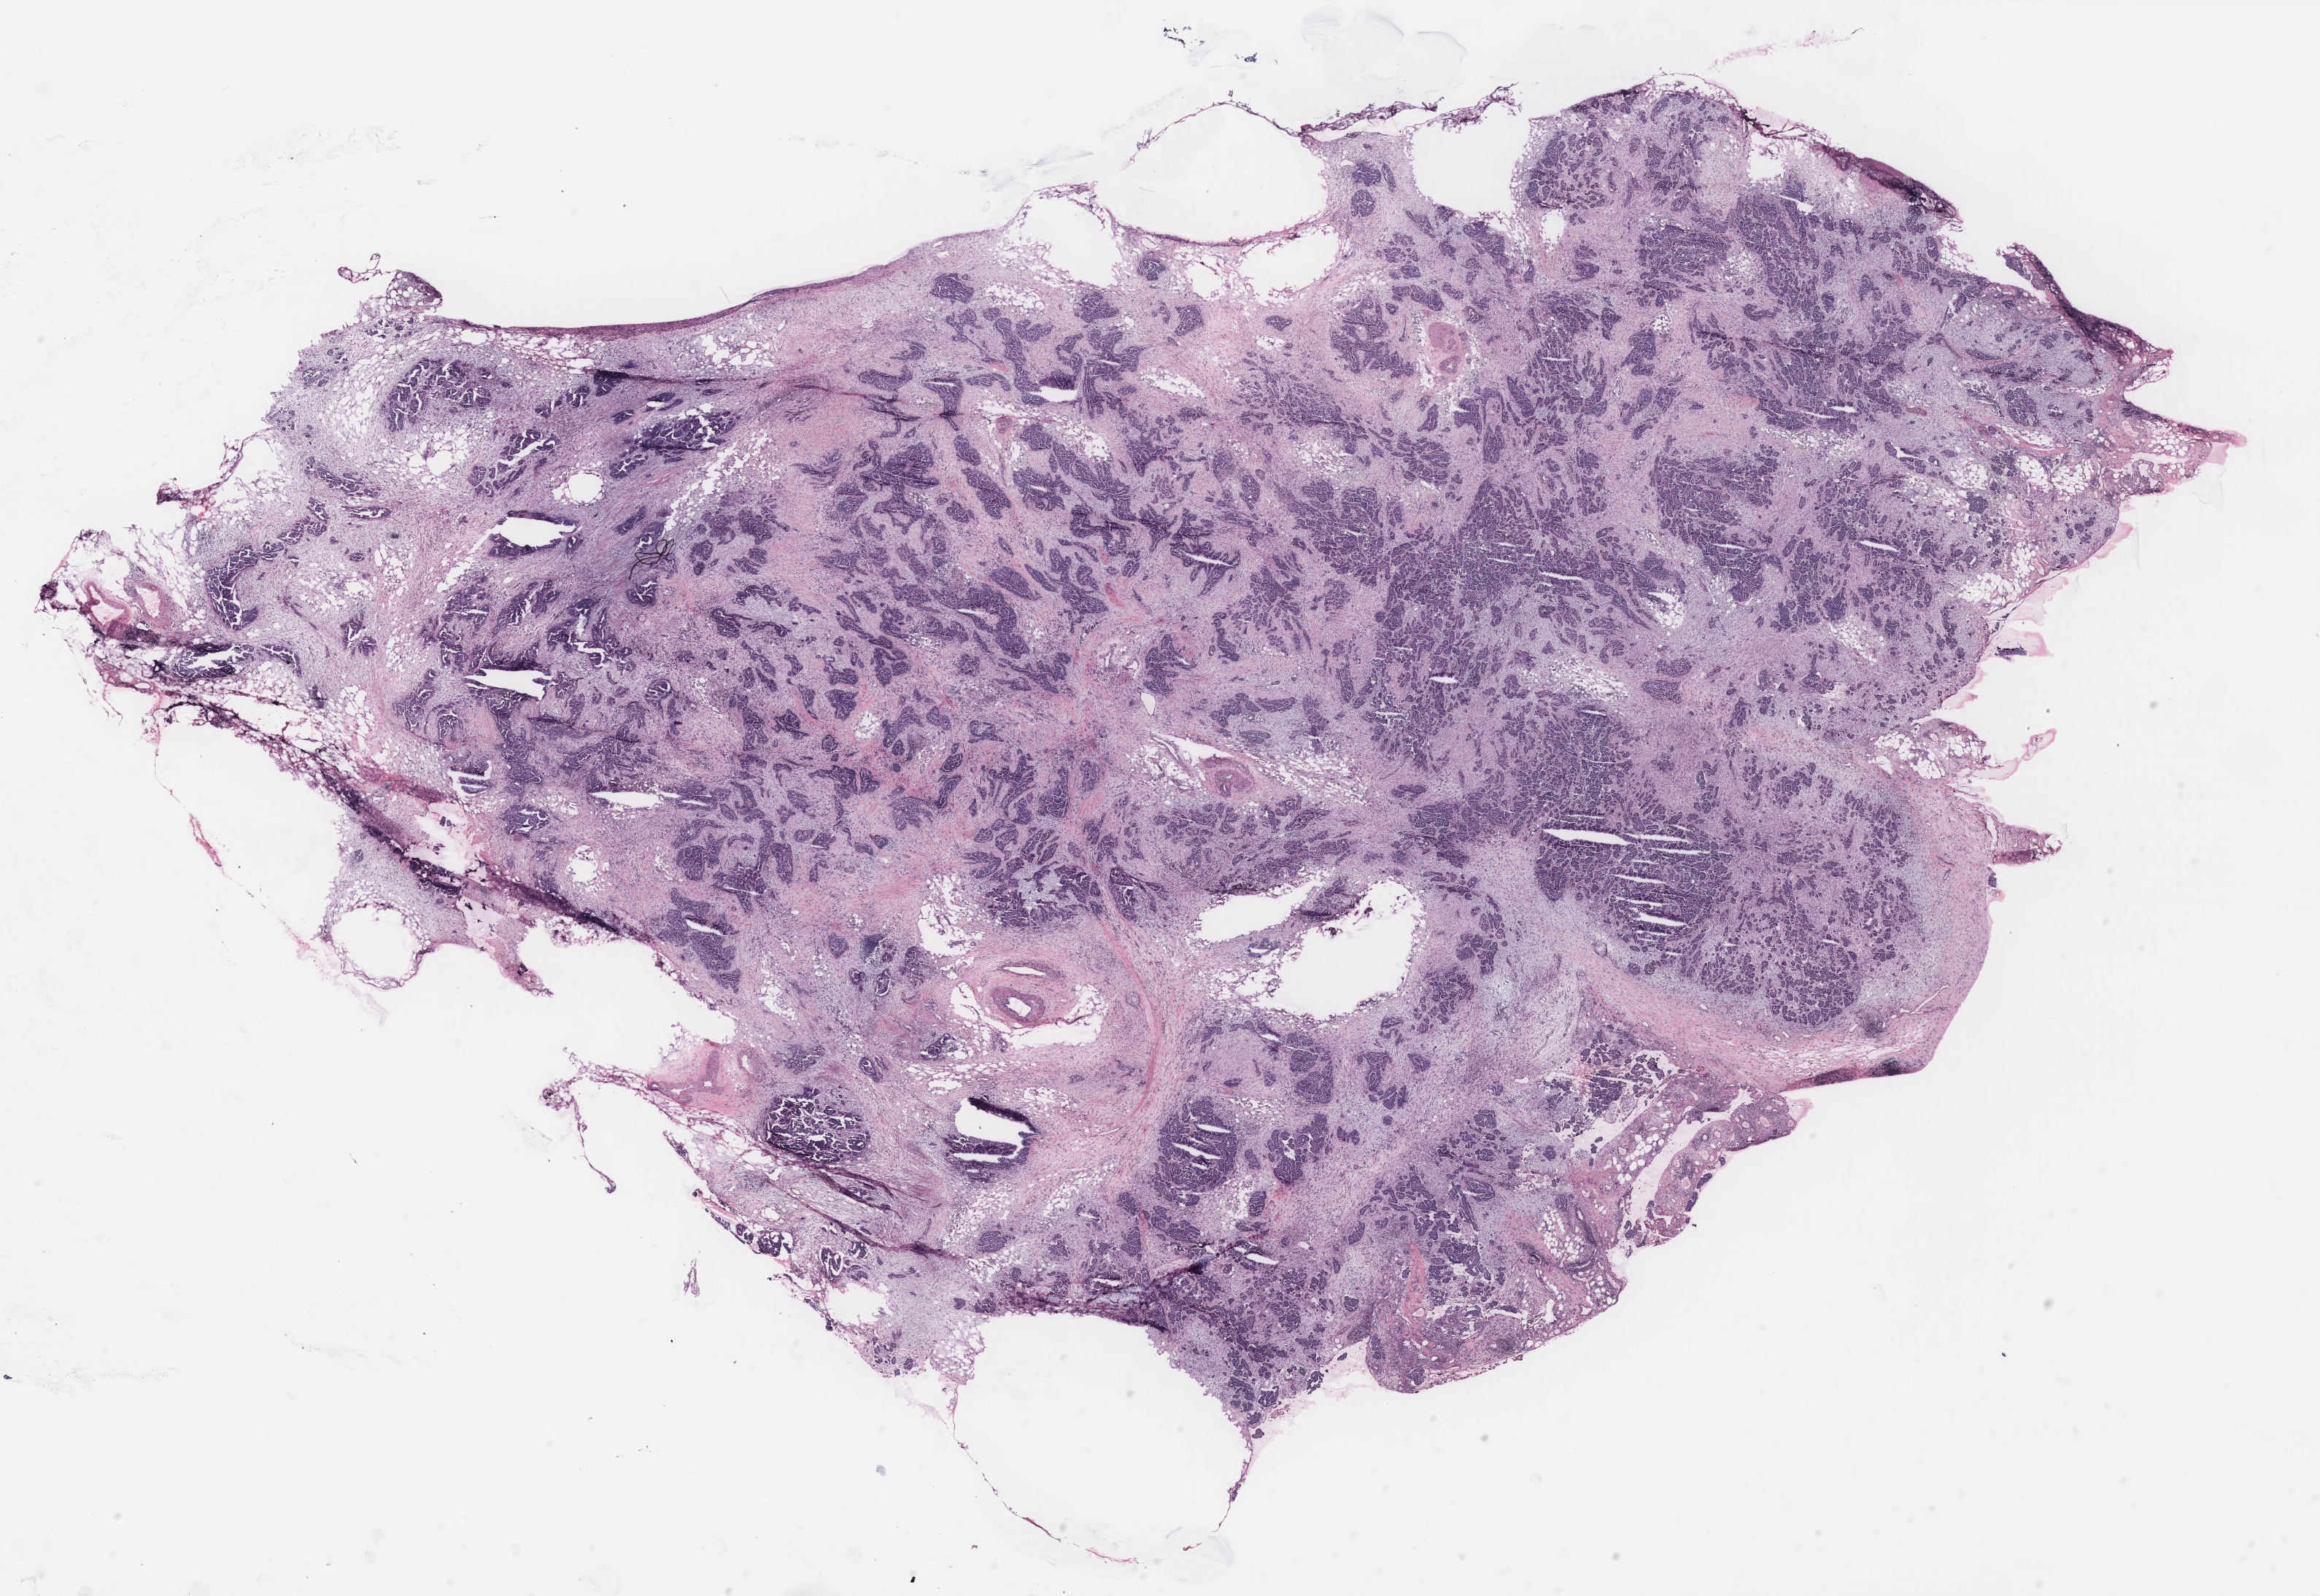
Hematoxylin and eosin (H&E) stained whole-slide image — low-resolution overview of the scanned area, about 25.5 x 17.5 mm (from a 40x scan); tumour tissue sample, ovary. 72-year-old female patient.
Primary tumour site (as recorded): fallopian tube. Histologic diagnosis: Serous adenocarcinoma, NOS (fallopian tube).